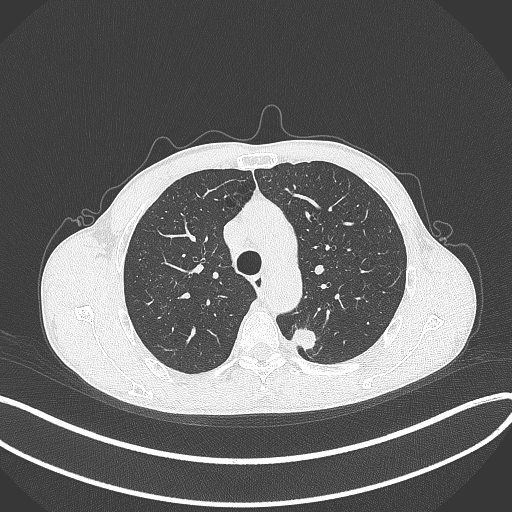
Chest CT, one axial slice; slice 287 of 429 in the series (ordered by position); reconstruction kernel B70f; lung window (W 1500 / L -600 HU); 512 × 512 image matrix, field of view 400 × 400 mm. Male patient, age 51 years. Case-level facts recorded for this patient, not image findings: clinical TNM (as recorded): T2a N1 M1.
Structures marked on this image (bounding box drawn by a radiologist):
- lung tumour (recorded histology: adenocarcinoma): bounding box (x1, y1, x2, y2) in pixels: (287, 326, 319, 353)